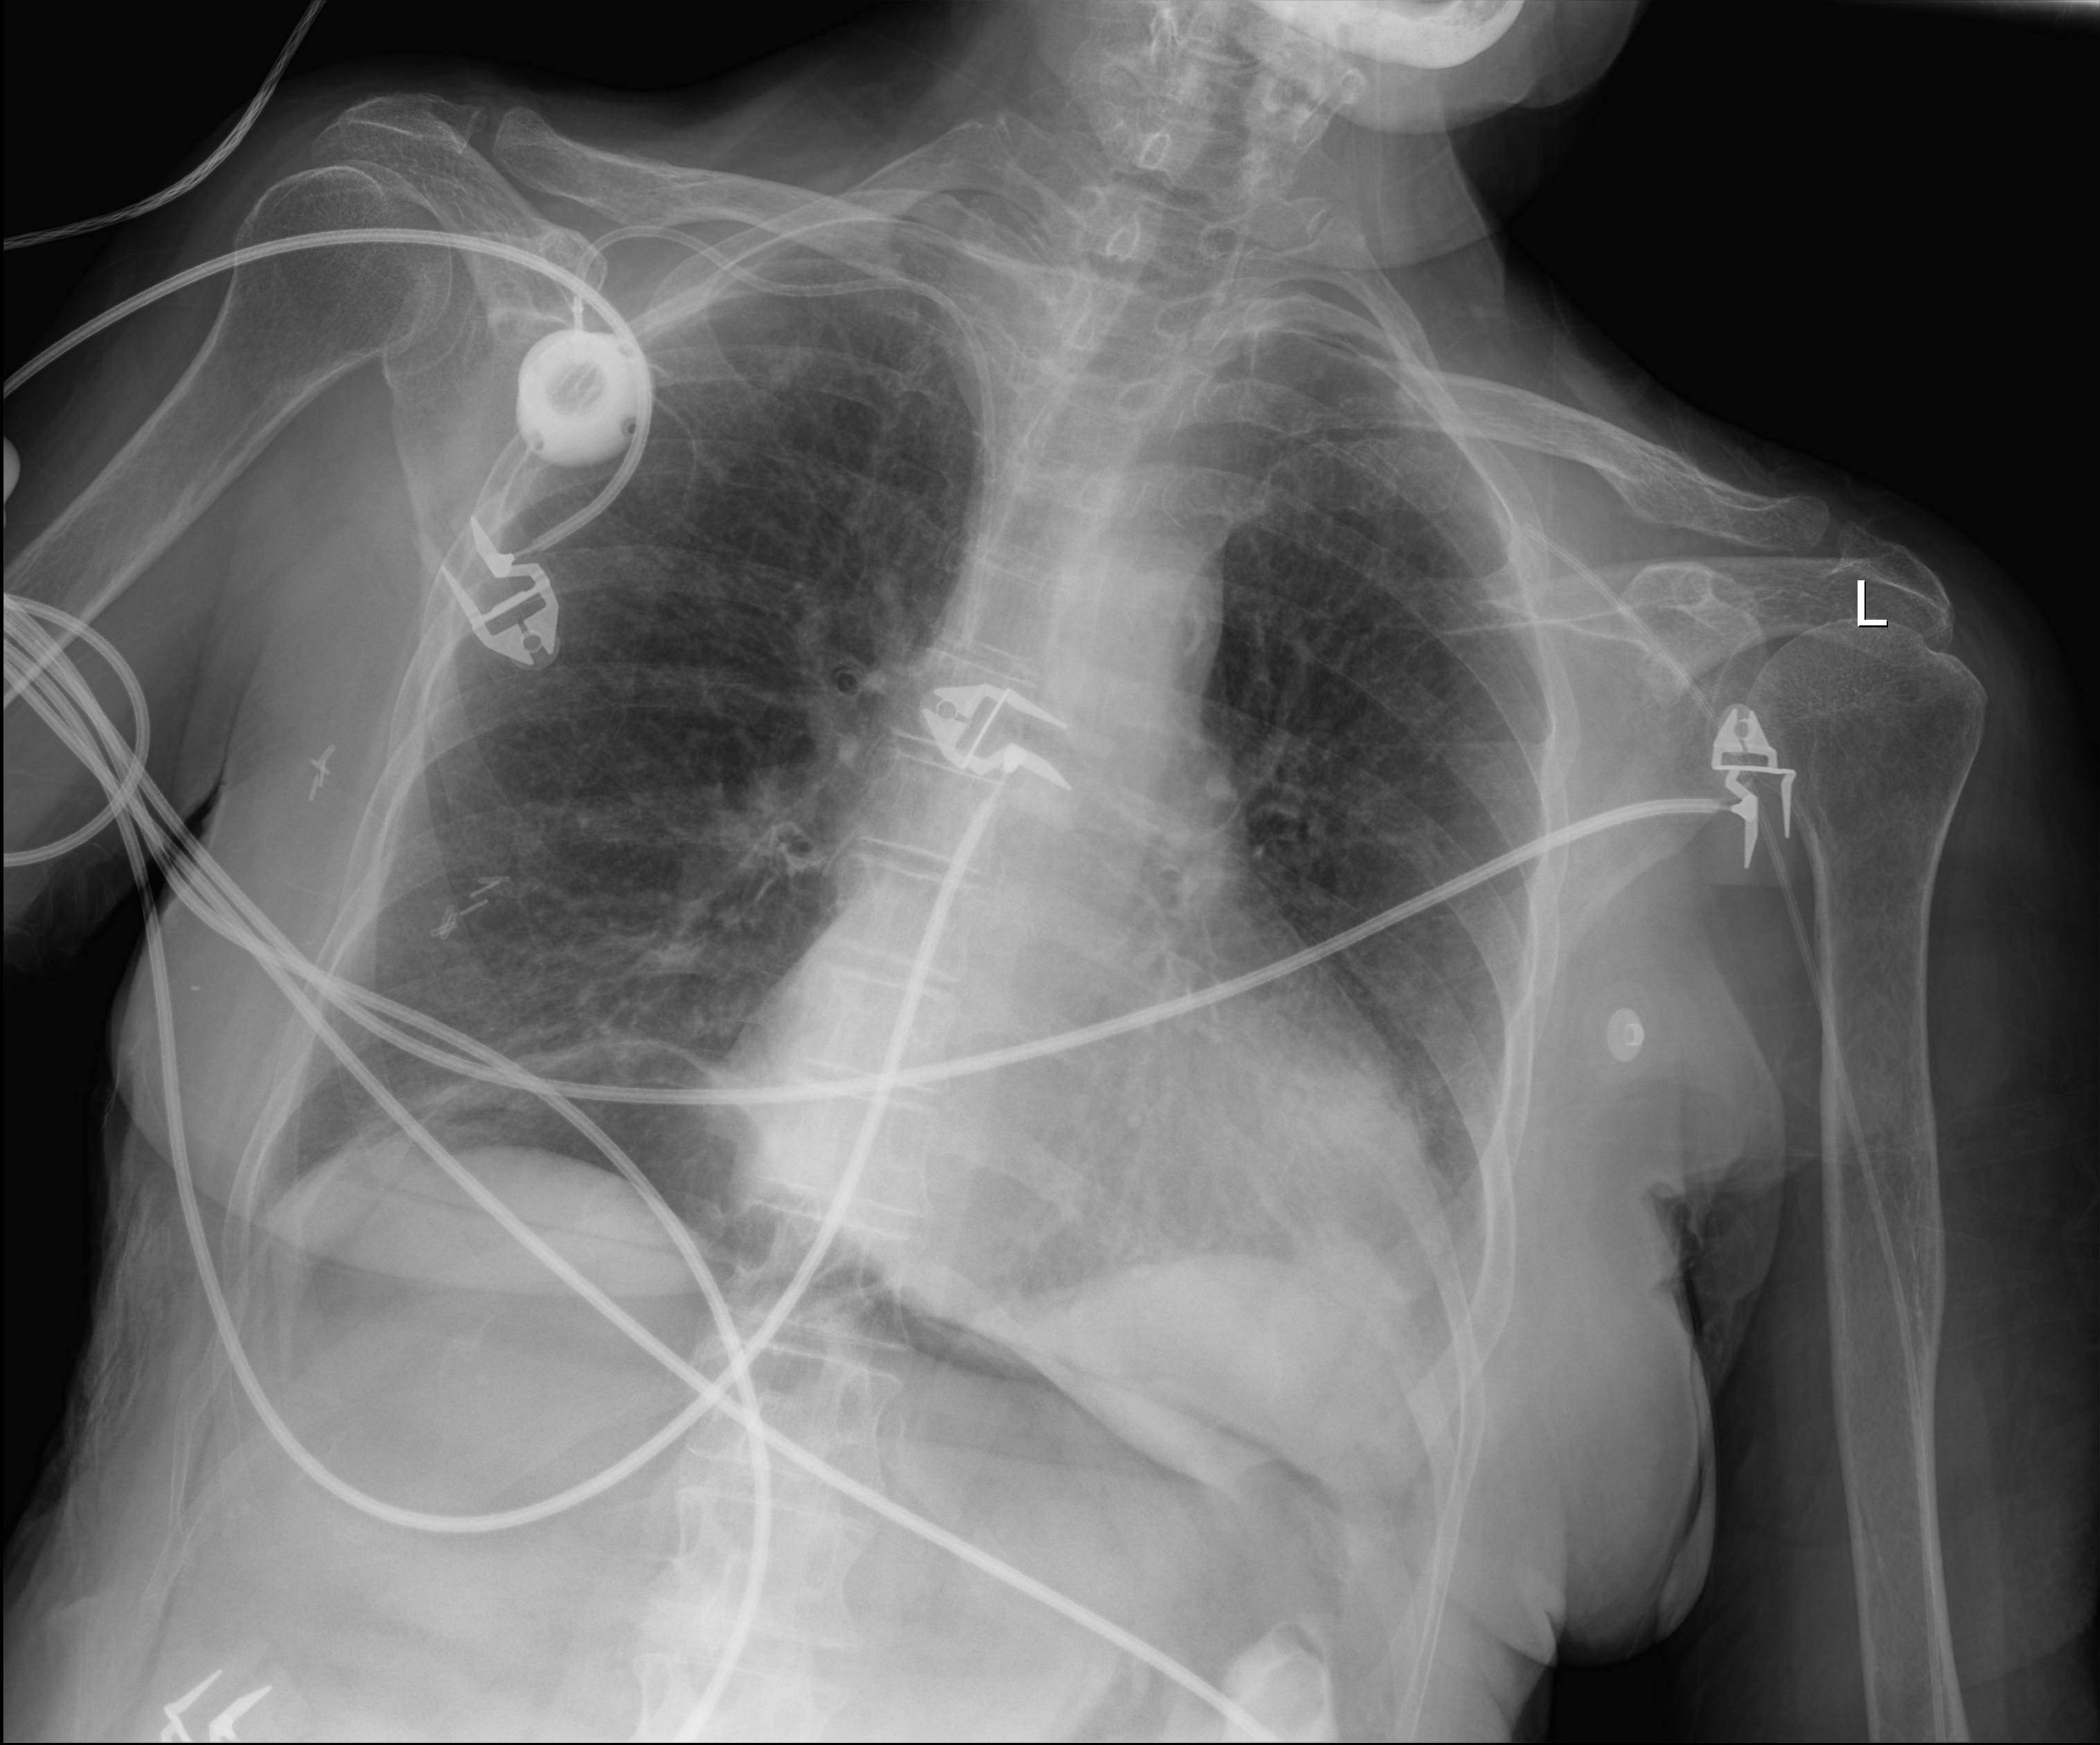
Chest X-ray (portable). Patient hospitalised with COVID-19; female, aged 60–74 years.
Hospital-stay facts (about this admission, not read from this image; timing relative to this image not recorded):
- admitted to intensive care during this hospital stay: yes
- mechanically ventilated during this hospital stay: yes